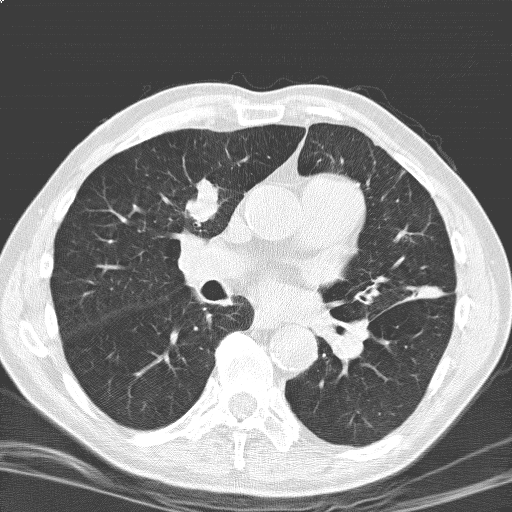
Low-dose screening chest CT, one axial slice; position 98 of 184 along the scan axis; 120 kVp; lung window (W 1500 / L -600 HU); 3.2 mm slice thickness; 512 × 512 image matrix, field of view 329 × 329 mm.
Structures marked on this image (manually delineated by an expert):
- lesion 1 (tumor, upper lobe of right lung): bounding box <186,180,218,223> (left, top, right, bottom; pixels)